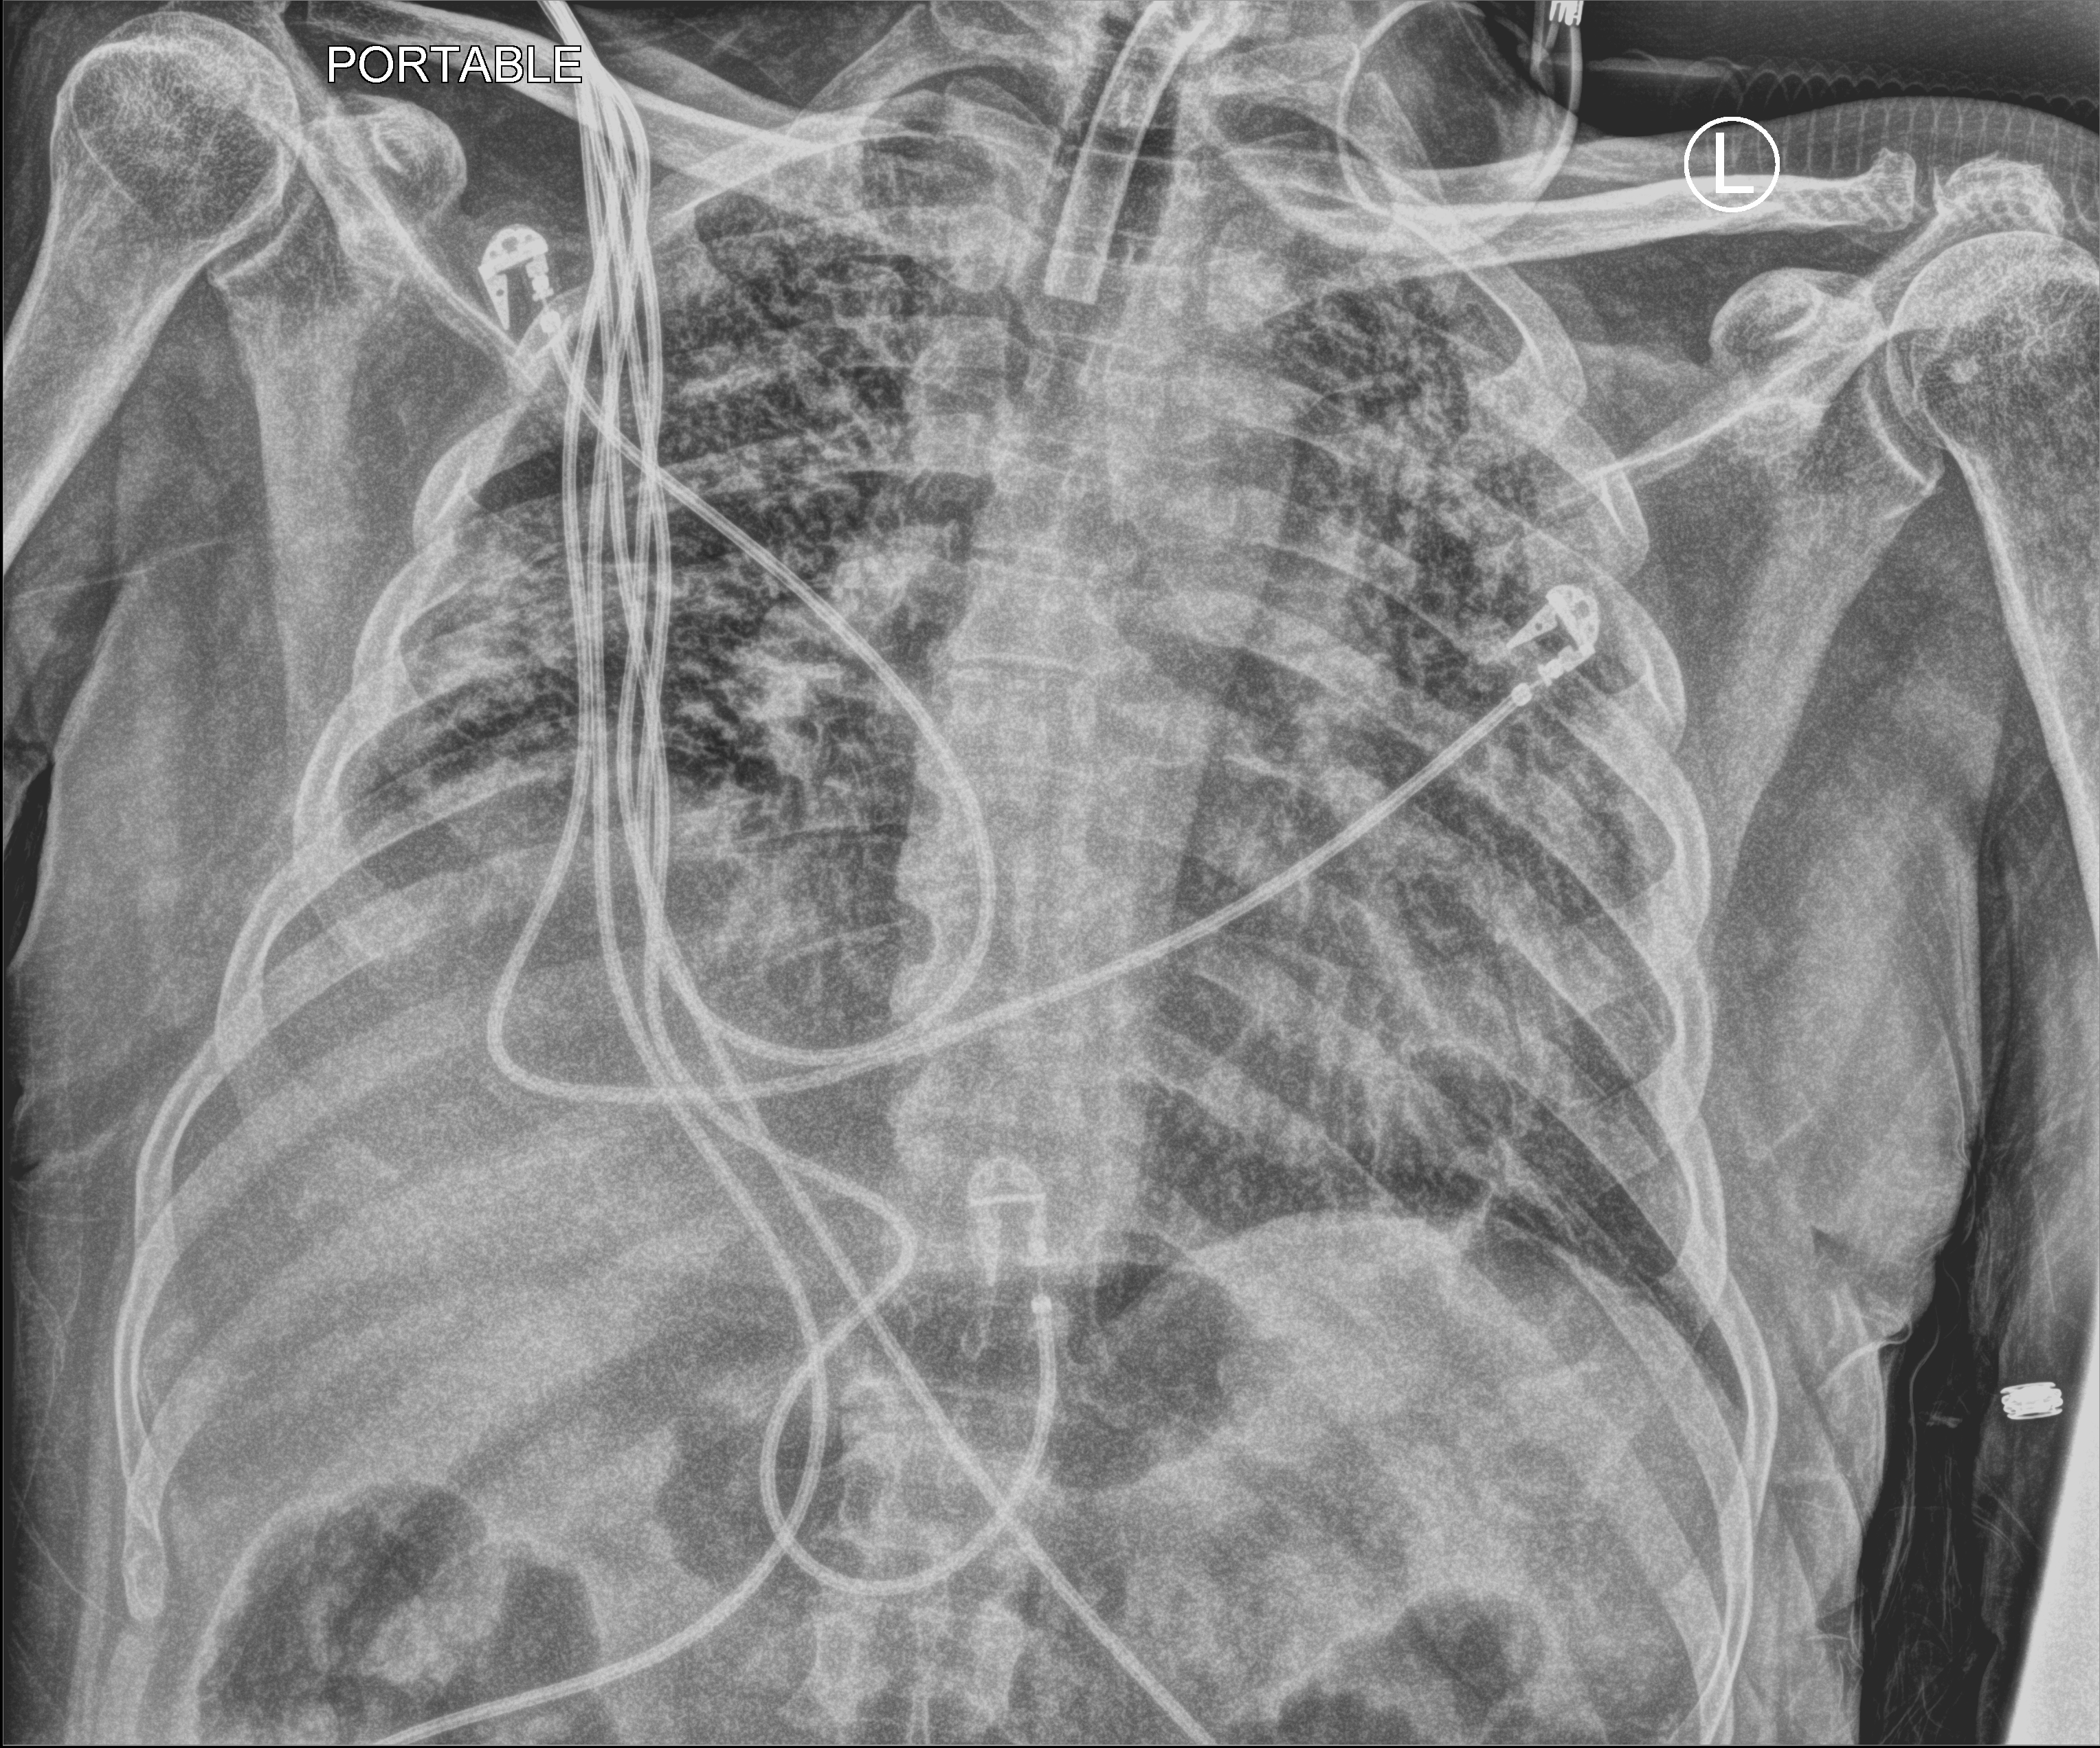
Portable chest radiograph. Male patient hospitalised with COVID-19, age 18–59 years.
Admission-level facts for this patient (not findings on this image; timing relative to this image not recorded): mechanically ventilated during this hospital stay: yes; admitted to intensive care during this hospital stay: yes.